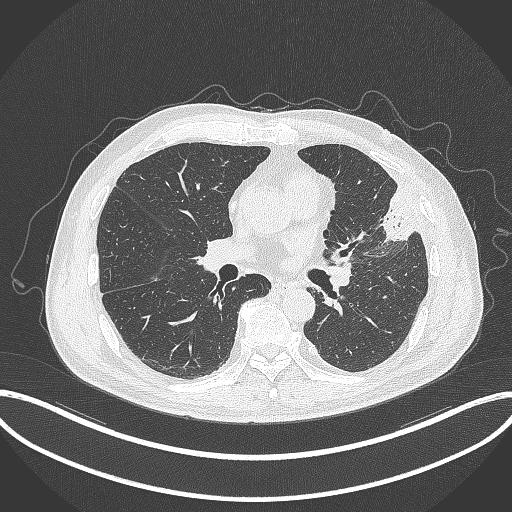
Chest CT, one axial slice; position 173 of 382 along the scan axis; reconstruction kernel B70f; 120 kVp; lung window (W 1500 / L -600 HU); 1 mm slice thickness; 512 × 512 image matrix, field of view 415 × 415 mm. Patient: male, 64 years. Case-level facts recorded for this patient, not image findings: clinical TNM (as recorded): T4 N1 M0; histopathological grade: G3.
Structures marked on this image (rectangle marked by the reading radiologist):
- lung tumour (recorded histology: adenocarcinoma): bounding box (x1, y1, x2, y2) in pixels: (366, 181, 422, 246)